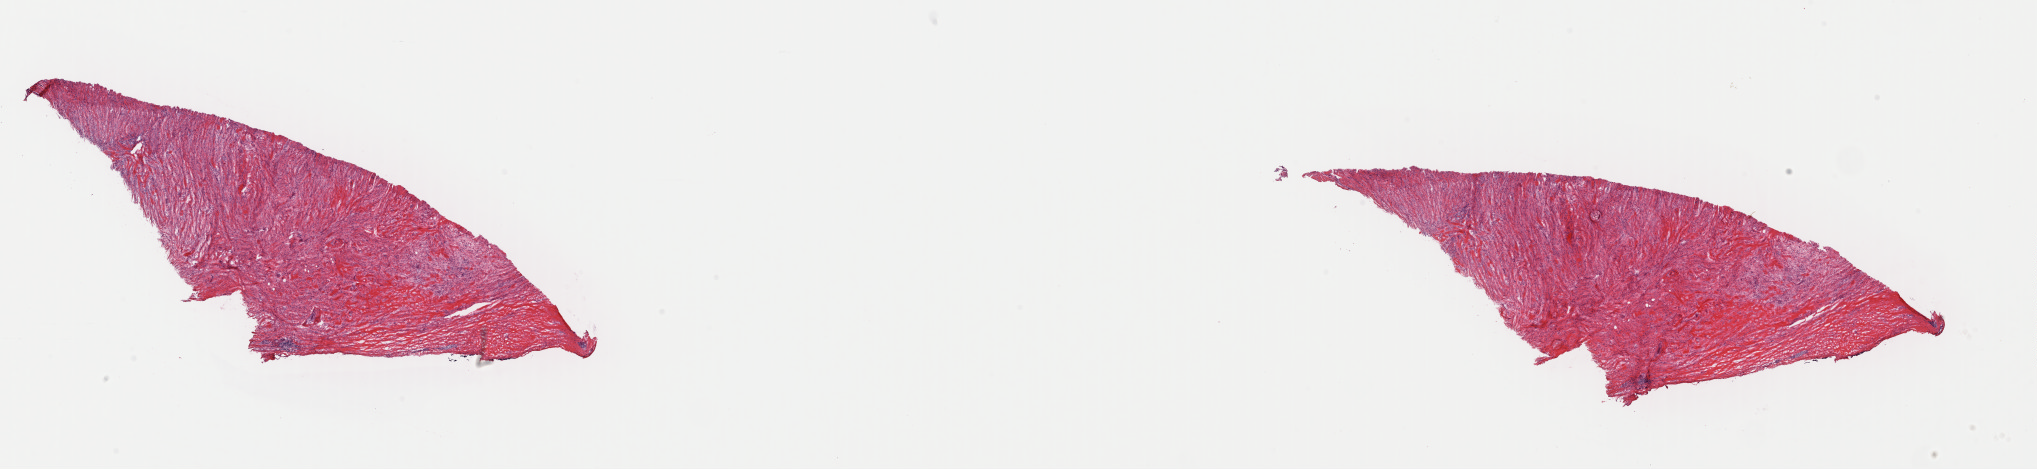
Digitized H&E-stained tissue section (whole slide) — shown as a low-resolution overview of the whole scanned area (about 32.2 x 7.4 mm, slide scanned at 40x). Frozen section from the top of the tissue portion. Primary tumour sample from the retroperitoneum and peritoneum. Patient: male, age at initial diagnosis 77 years. Slide review estimates, as recorded: tumour cells 85%, tumour nuclei 95%, normal cells 0%, stromal cells 15%, necrosis 0%. Inflammatory infiltration, as recorded: lymphocyte infiltration 0%, monocyte infiltration 0%, neutrophil infiltration 0%.
Pathologic diagnosis: Dedifferentiated liposarcoma (retroperitoneum).